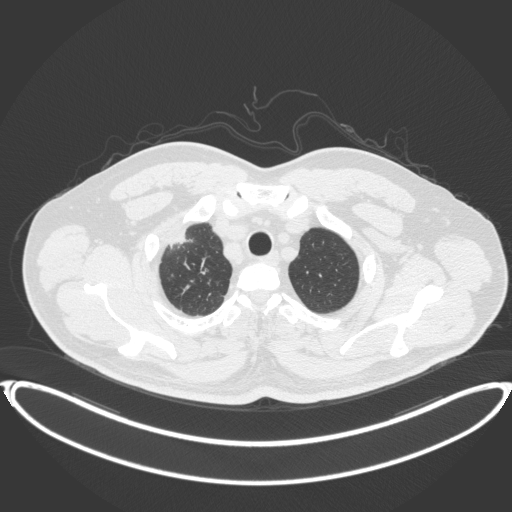
Chest CT, one axial slice; slice 345 of 399 in the series (ordered by position); 120 kVp; lung window (W 1500 / L -600 HU); 1 mm slice thickness; 512 × 512 image matrix, field of view 445 × 445 mm. Male patient, age 53 years. Case-level facts recorded for this patient, not image findings: clinical TNM (as recorded): T2a N0 M0.
Annotated regions visible in this slice (bounding box drawn by a radiologist):
- lung tumour (recorded histology: adenocarcinoma): box from (x=166, y=226) to (x=198, y=253) px